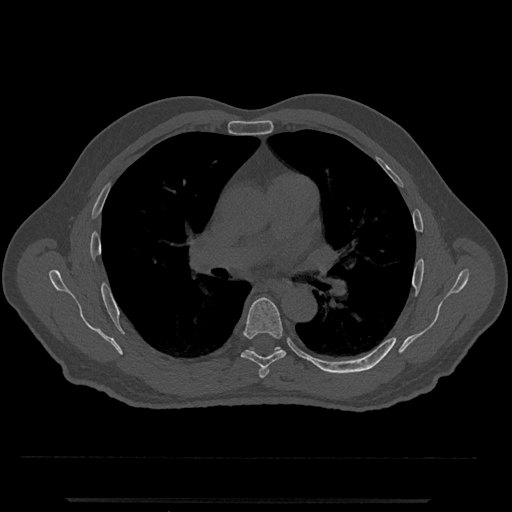
CT including the spine, one axial slice; position 733 of 797 along the scan axis; bone window (W 1800 / L 400 HU); 0.5 mm slice thickness; 512 × 512 image matrix. Patient: male, 63 years. Case-level facts recorded for this patient, not image findings: primary cancer: prostate.
Structures marked on this image (semi-automatically segmented with operator editing):
- T5 vertebra: bounding box [x1, y1, x2, y2] px = [258, 367, 269, 378]
- T6 vertebra: [241, 297, 286, 369]
- T7 vertebra: [249, 346, 281, 351]